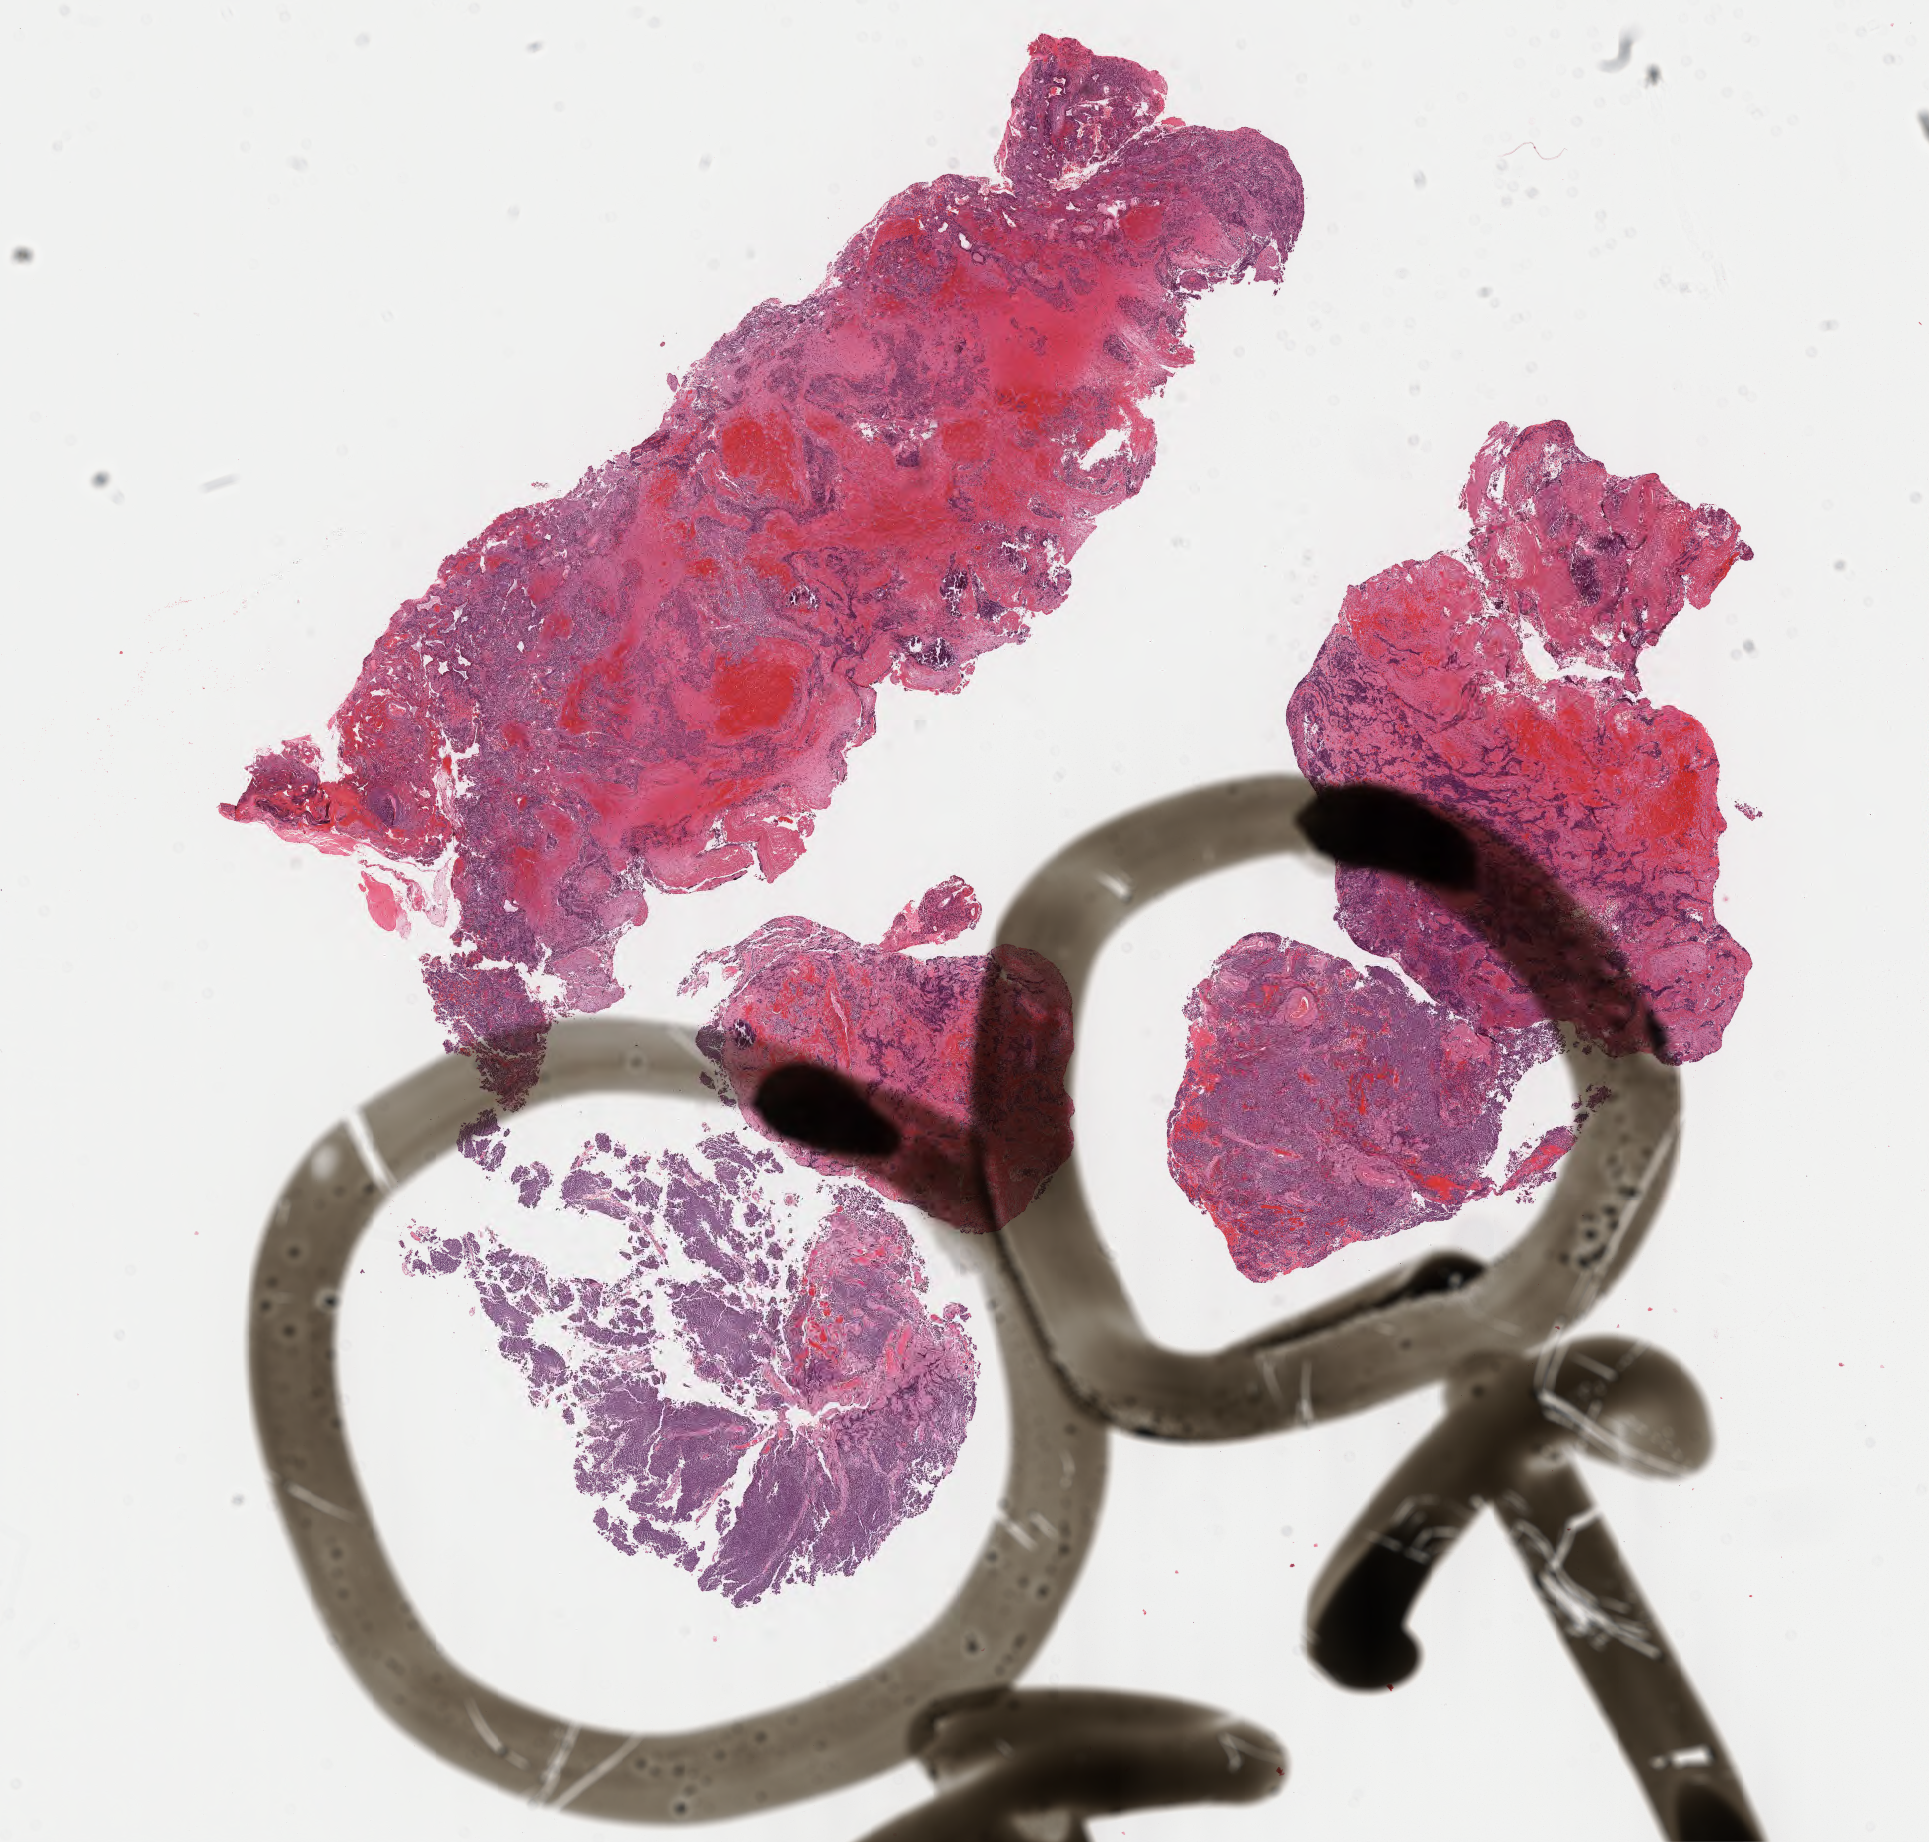
Whole-slide image, haematoxylin and eosin stain of tumor tissue from the brain — a low-resolution overview of the entire scanned area, about 15.6 x 14.9 mm, FFPE section. Male patient, age 59 months (4 years 11 months).
Diagnosis (ICD-O-3 morphology term): CNS embryonal tumor, NOS.